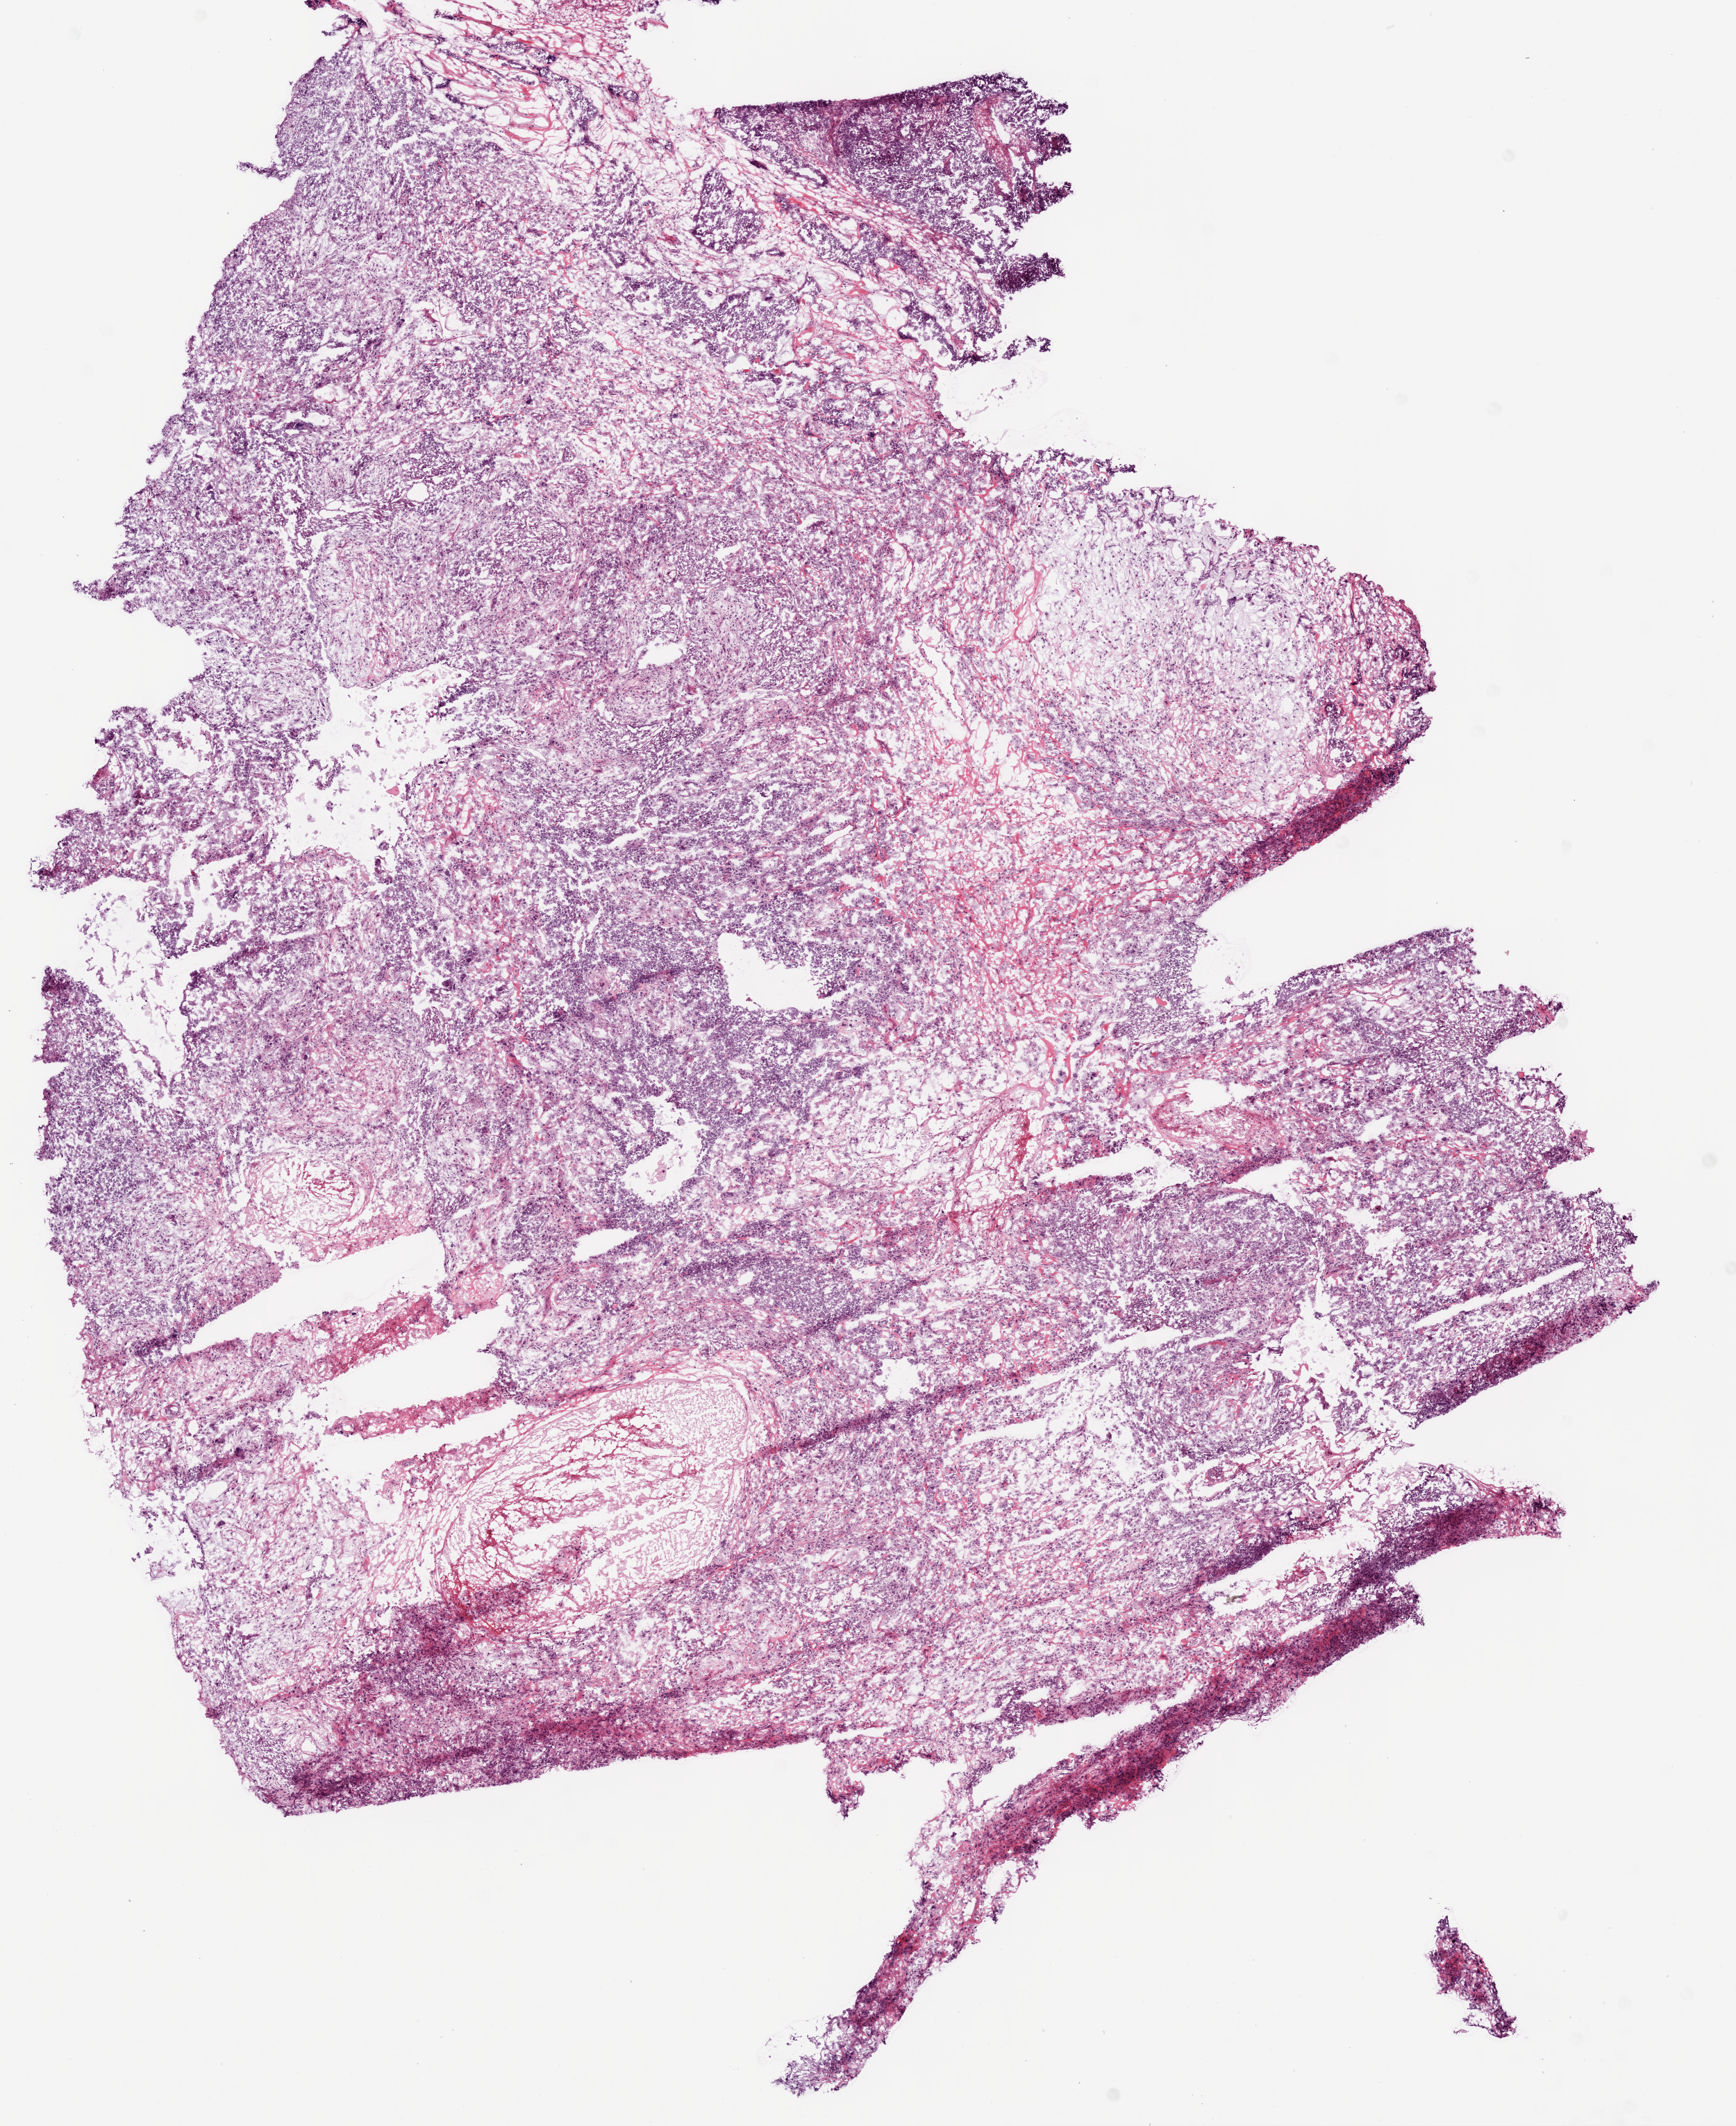
Whole-slide histology image, H&E, a low-resolution overview of the entire scanned area, about 10.0 x 12.3 mm (from a 20x scan); frozen section from the bottom of the tissue portion; primary tumour sample from the ovary. Female patient; age at initial diagnosis 49 years. Histologic grade: G3 (poorly differentiated). Pathologist review of this section (percent, as recorded): tumour cells 80%, tumour nuclei 85%, normal cells 0%, stromal cells 10%, necrosis 10%.
Histologic diagnosis: Serous cystadenocarcinoma, NOS. Laterality: left. FIGO stage: IIIC.